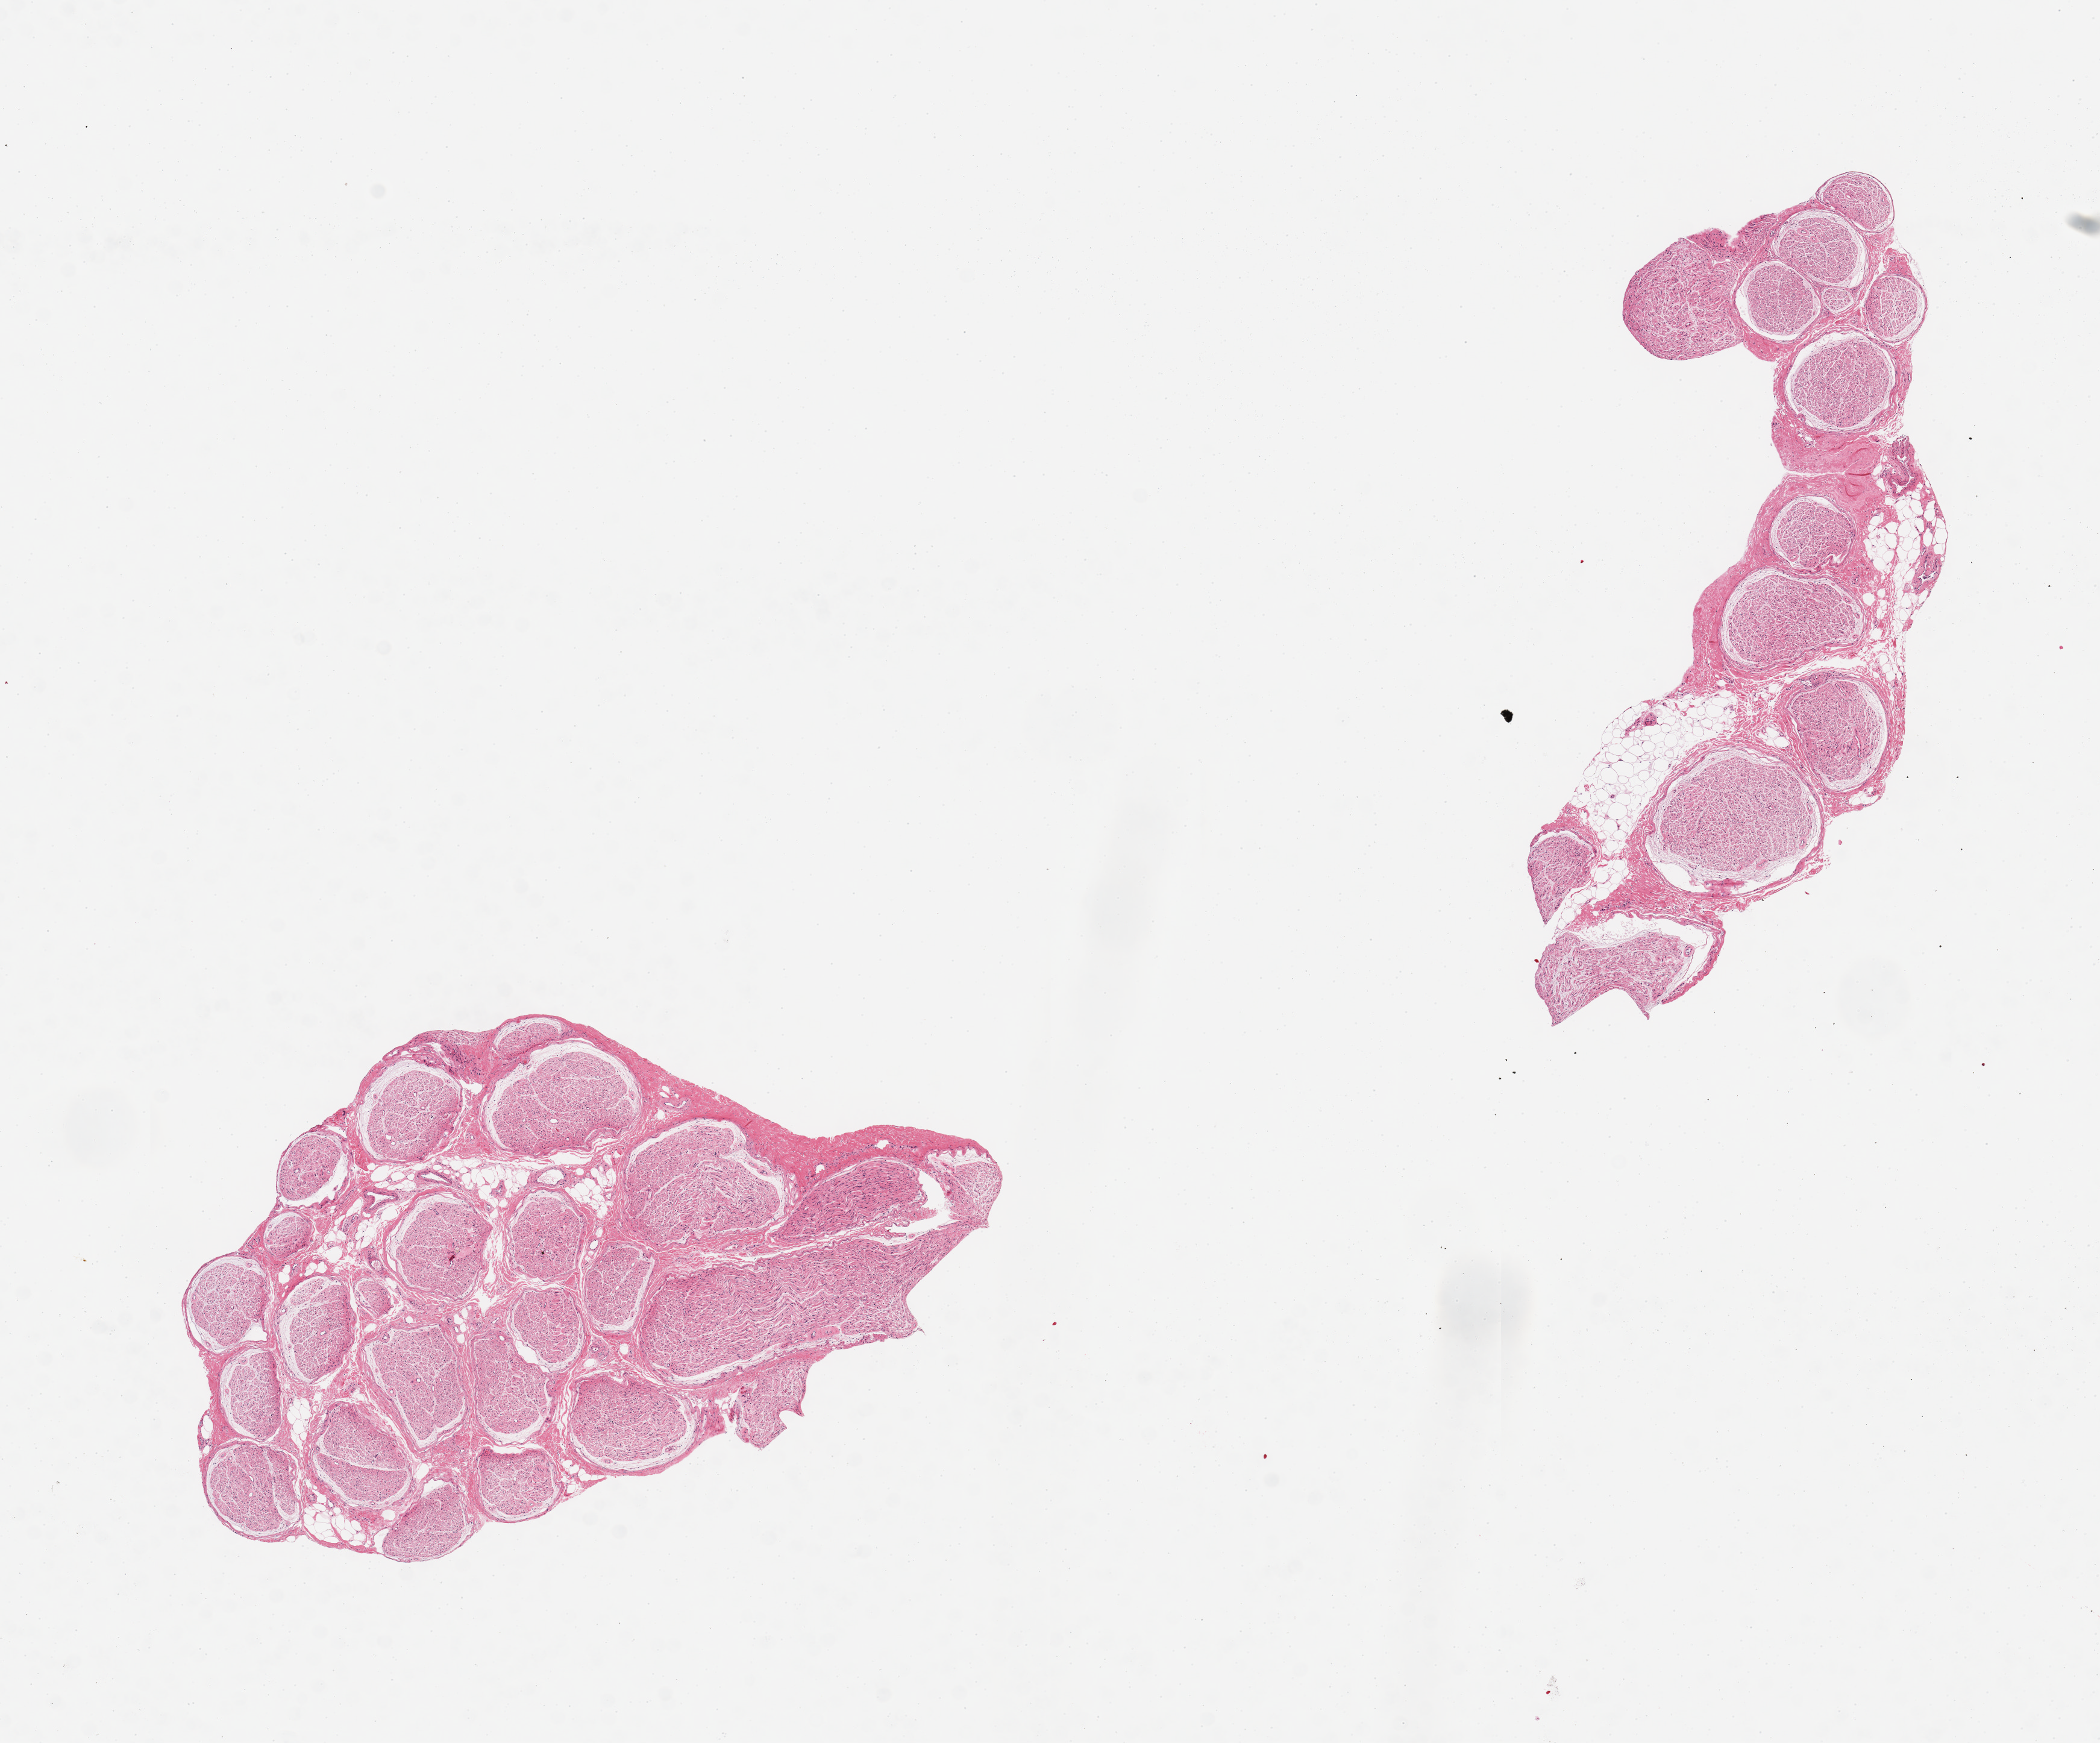
Whole-slide image, H&E stain, shown as a low-resolution overview of the whole scanned area (about 13.8 x 11.4 mm), PAXgene-fixed, paraffin-embedded tissue, target tissue: tibial nerve, tissue donor sample. Donor sex: male.
Pathologist's review note for this sample: 2 pieces; up to 10% fat content; small arteries hyalinized.